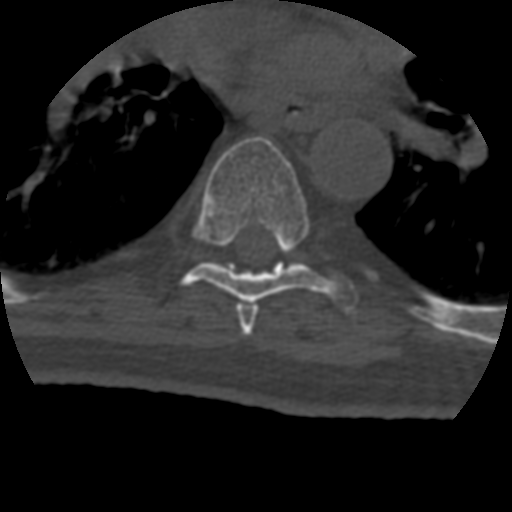
CT including the spine, one axial slice. Position 281 of 399 along the scan axis. Reconstruction kernel STANDARD. 120 kVp. Bone window (W 1800 / L 400 HU). 512 × 512 image matrix, field of view 160 × 160 mm. Patient age 69 years. Case-level facts recorded for this patient, not image findings: primary cancer: prostate.
Structures marked on this image (semi-automatically segmented with operator editing):
- T6 vertebra: box from (x=236, y=303) to (x=258, y=337) px
- T7 vertebra: (x=183, y=137)–(x=358, y=311)